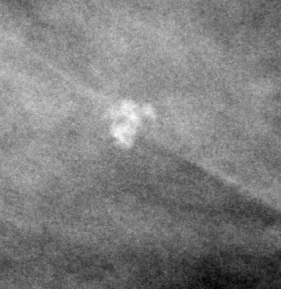
Region of interest cut from a scanned film mammogram (one marked finding); right breast; CC view.
Marked abnormality: calcifications, morphology dystrophic, distribution clustered; BI-RADS assessment category 3; pathology (as recorded): benign.